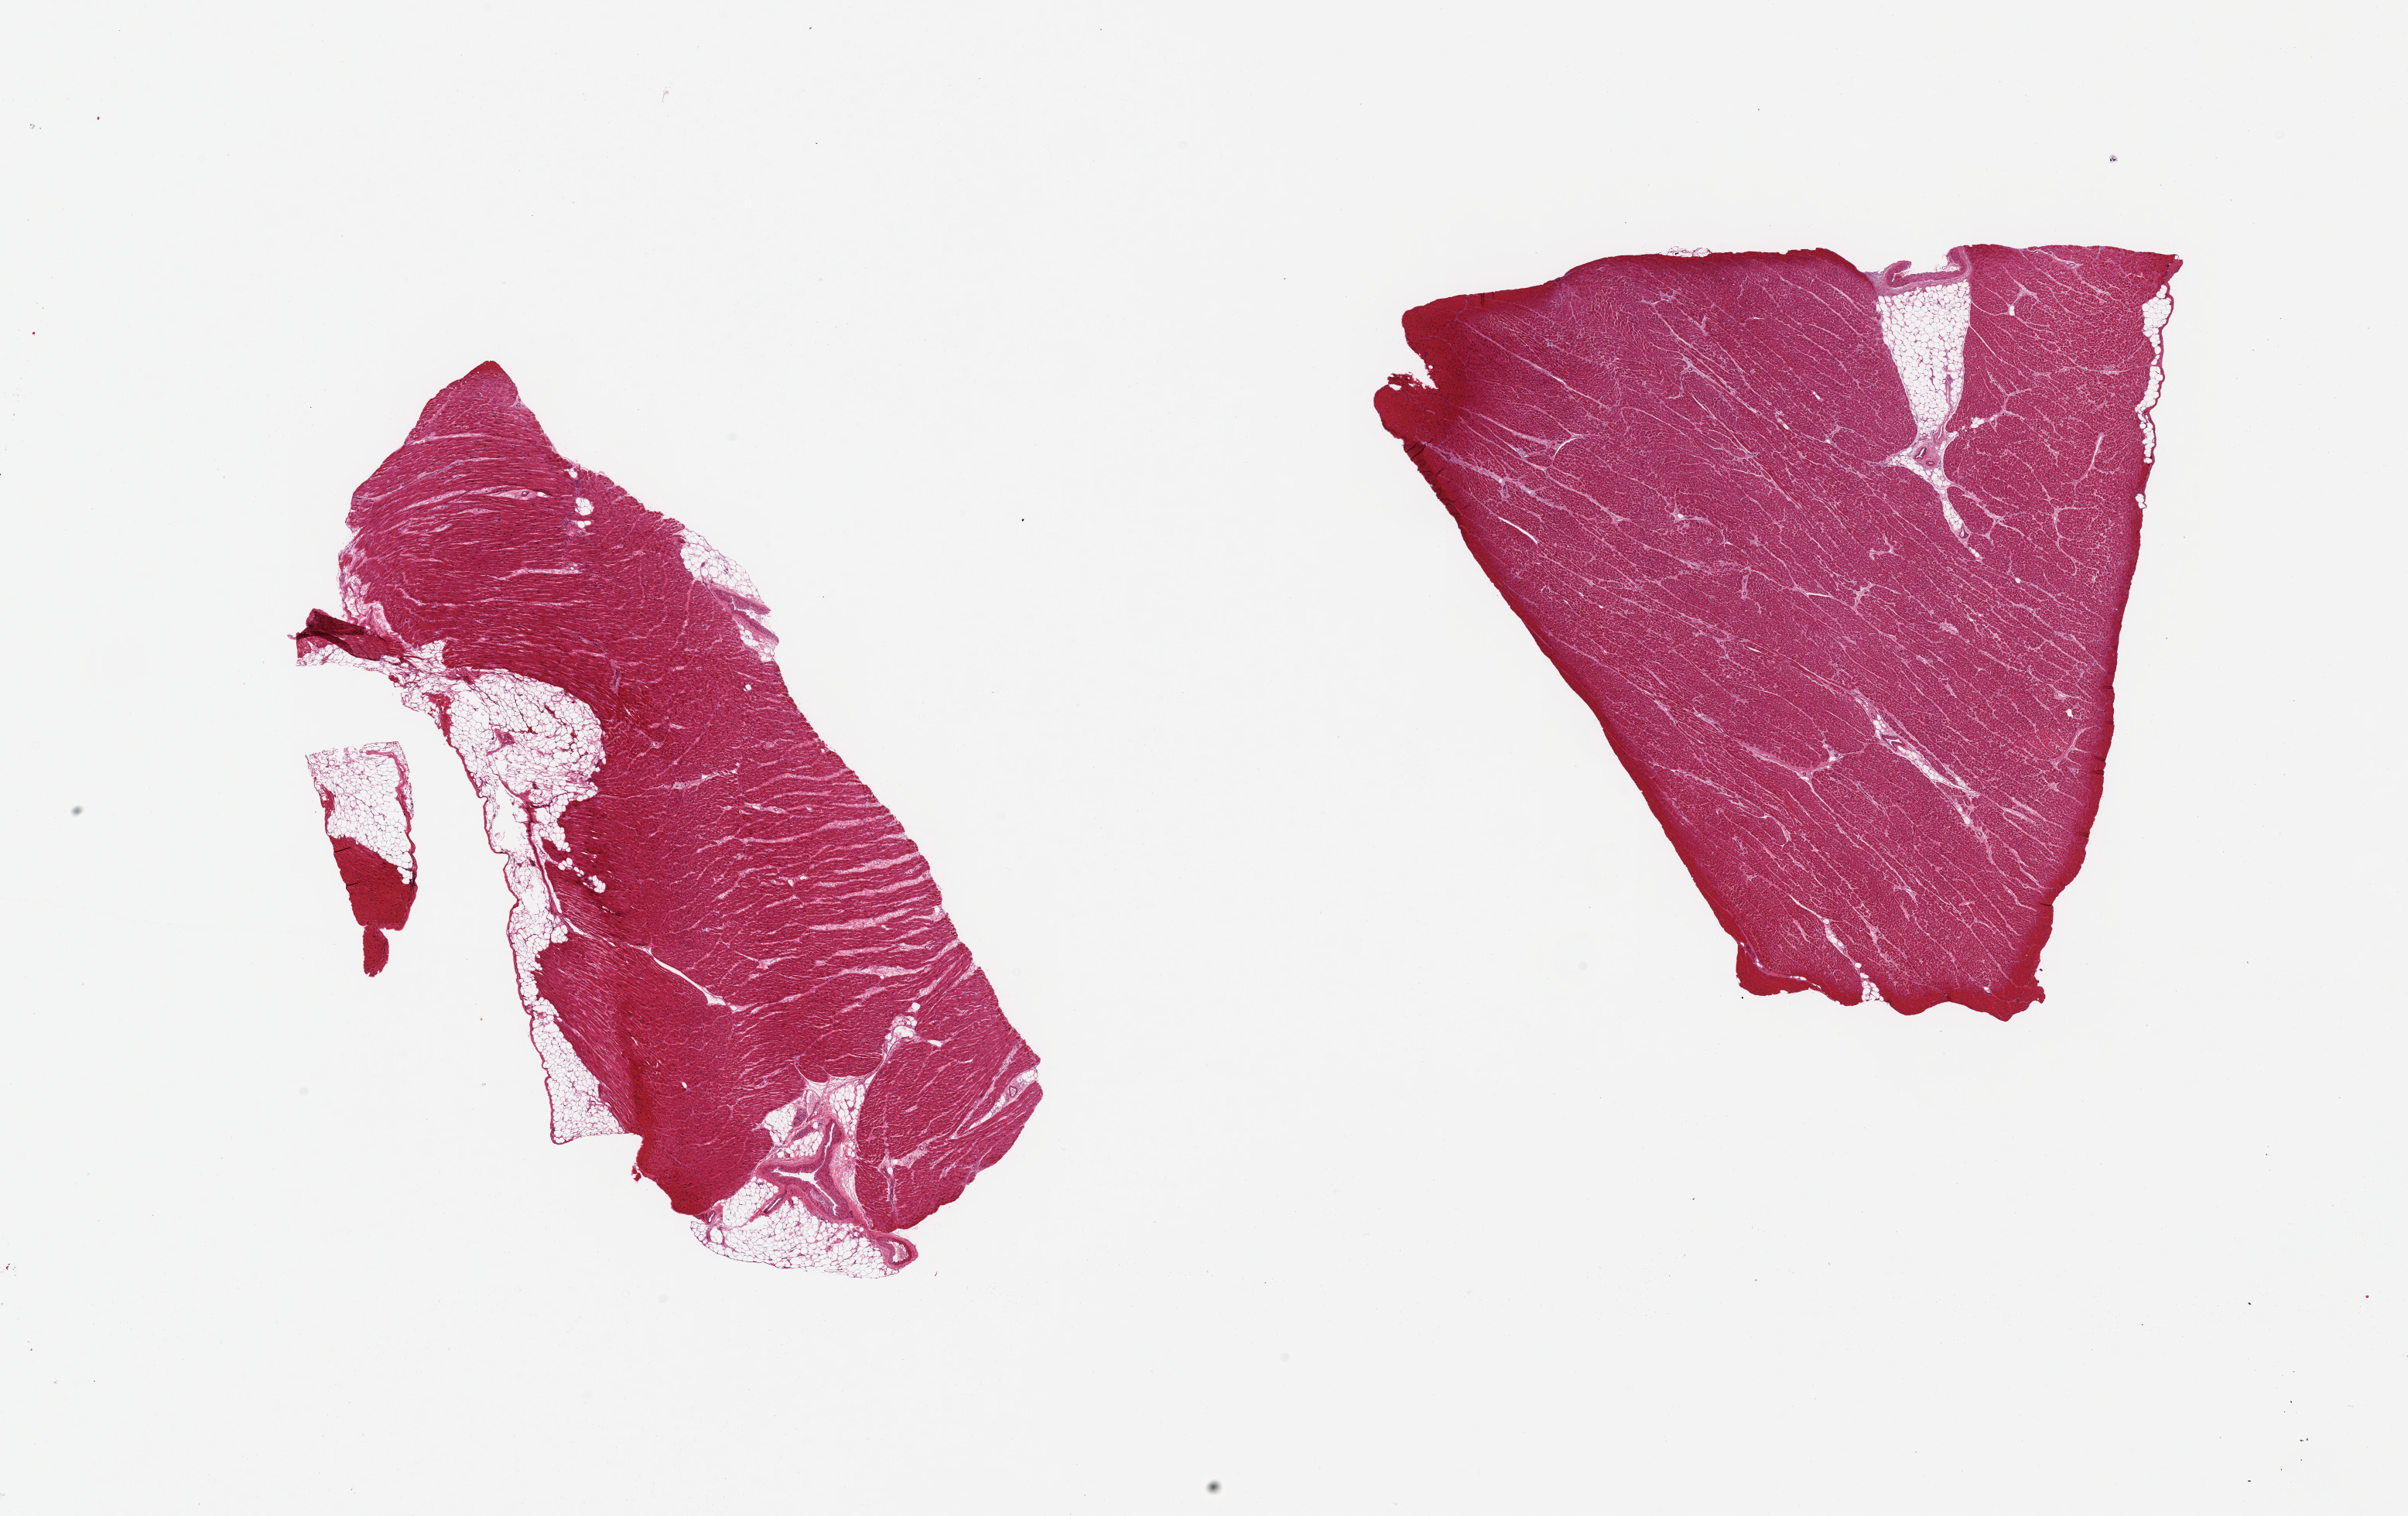
Haematoxylin and eosin whole-slide image, brightfield — low-resolution overview of the scanned area, about 24.6 x 15.5 mm (from a 20x scan). PAXgene-fixed paraffin-embedded (PFPE) section. Sampled site (target tissue): heart. Donor tissue sample. Donor: male.
- review note (as recorded): 2 pieces, mild interstitial fibrosis/chronic ischemic changes